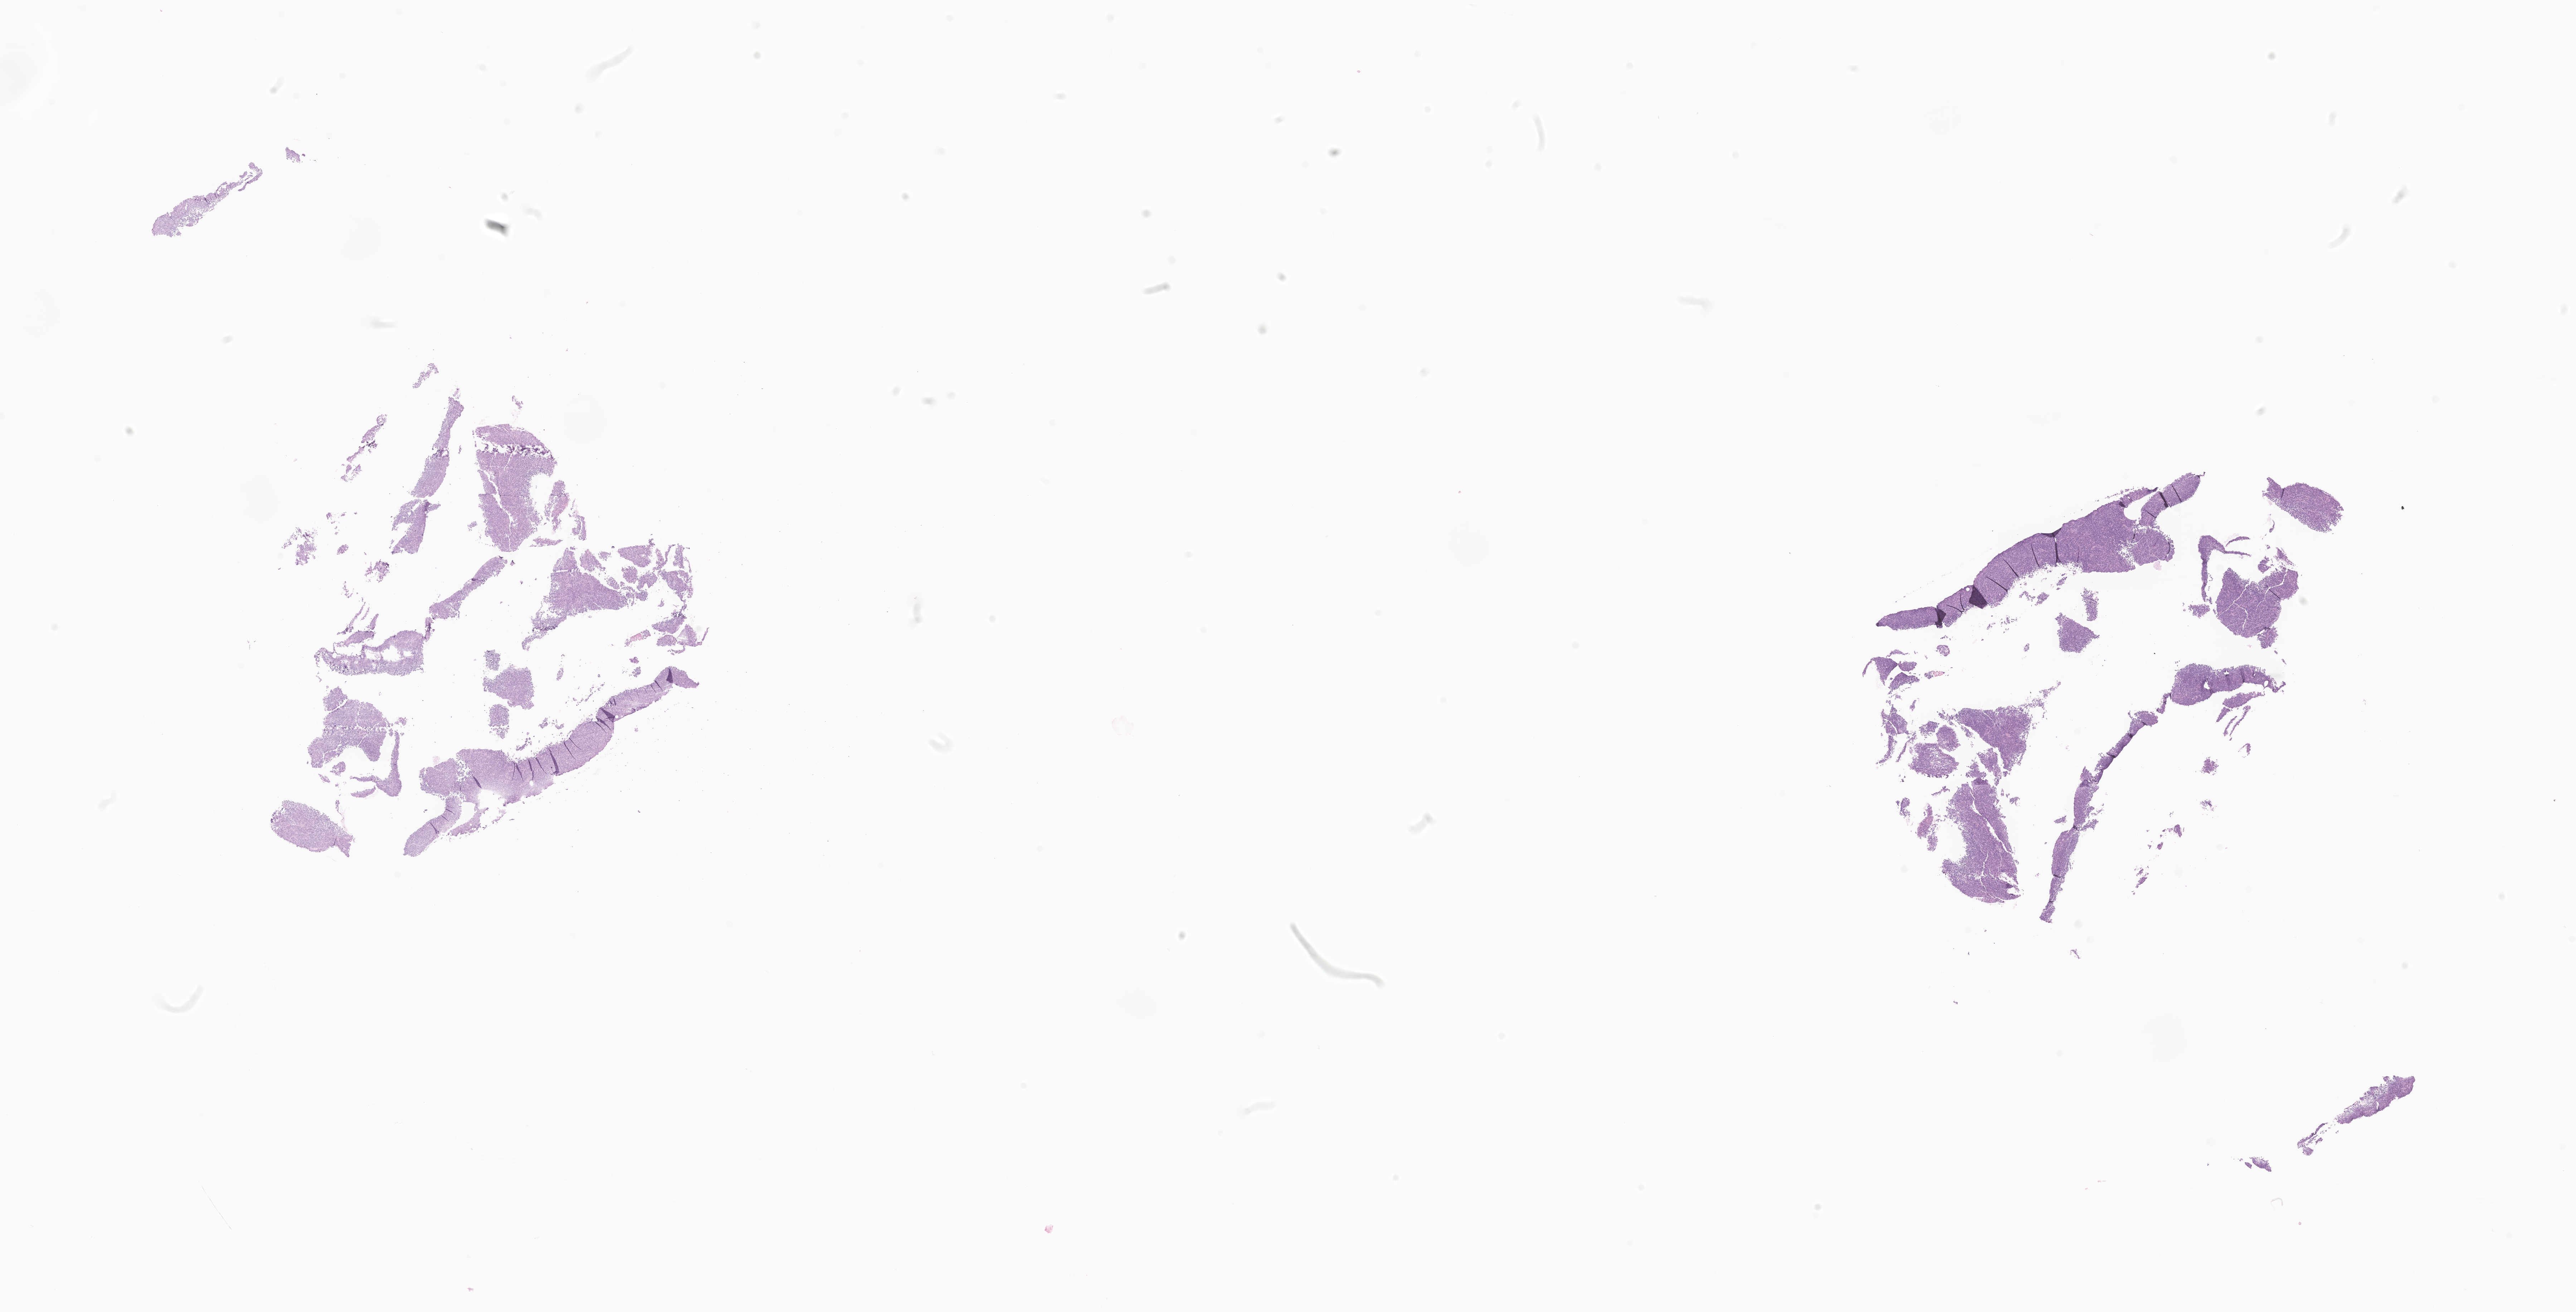
Whole-slide image, haematoxylin and eosin stain of tumor tissue from the brain stem, whole scanned area (about 30.3 x 15.5 mm) shown as a low-resolution overview; FFPE section. Patient female; age 123 months (10 years 3 months).
Recorded diagnosis: Glioma, malignant.